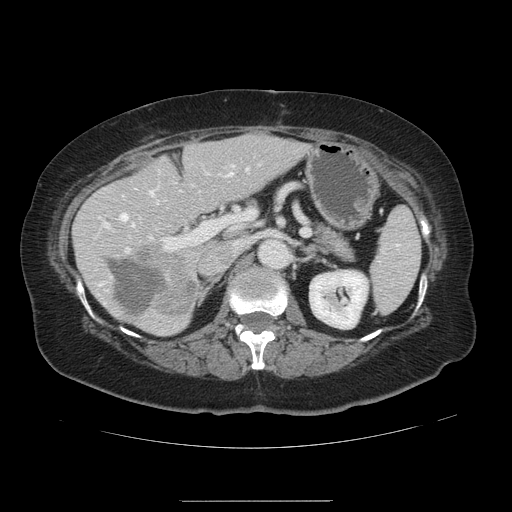
Contrast-enhanced abdominal CT, one axial slice. Slice 70 of 141 in the series (ordered by position). Intravenous contrast given. Soft-tissue window (W 400 / L 40 HU). 2.5 mm slice thickness. 512 × 512 image matrix, field of view 393 × 393 mm. Female patient, age 74 years. From the clinical record (not read from this slice): diagnosis: colorectal cancer liver metastases, imaged before liver resection; multiple liver metastases: yes; largest metastasis: 7 cm; disease in both lobes: yes.
Structures marked on this image (outlined manually by an expert reader):
- hepatic veins: bounding box [x1, y1, x2, y2] px = [120, 173, 232, 229]
- liver: [74, 135, 304, 334]
- planned liver remnant (the part of the liver to remain after resection): [75, 135, 304, 334]
- portal vein (with intrahepatic branches): [98, 164, 248, 253]
- liver metastasis: [109, 260, 165, 315]
- liver metastasis: [134, 244, 194, 316]